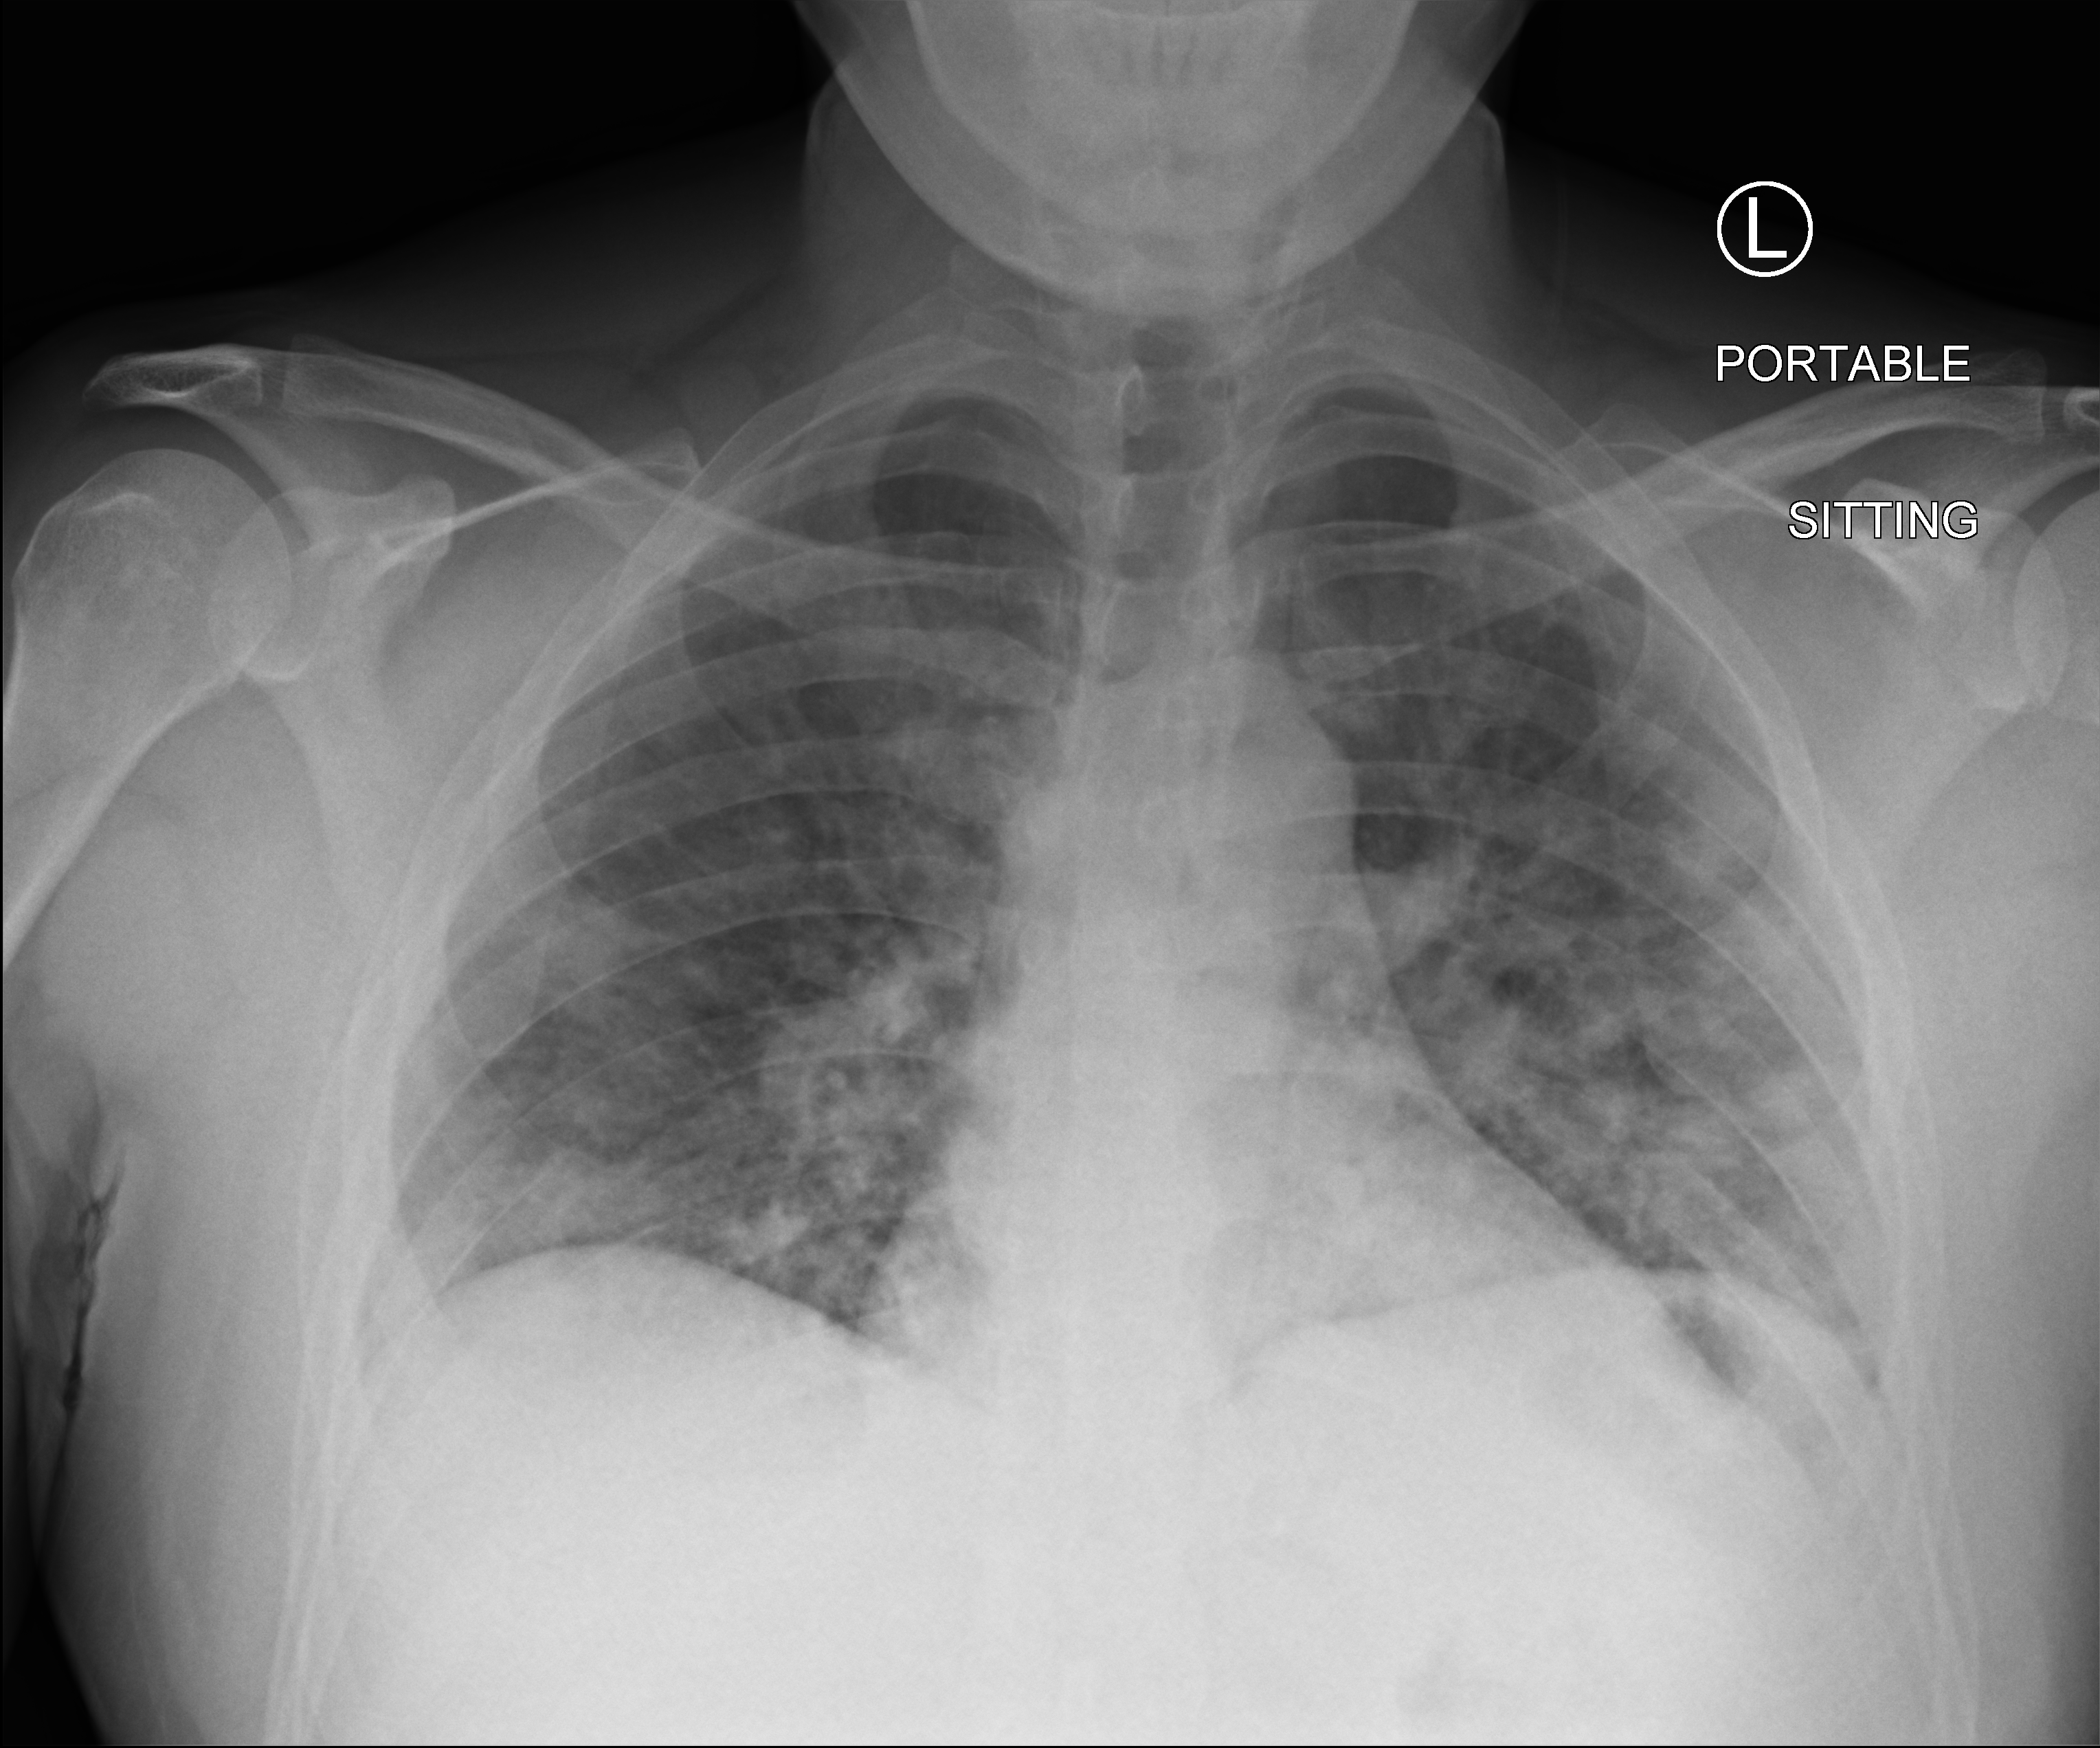
Portable chest radiograph; anteroposterior (AP) projection. Male patient hospitalised with COVID-19, age 18–59 years.
Admission-level facts for this patient (not findings on this image; timing relative to this image not recorded):
- admitted to intensive care during this hospital stay: no
- mechanically ventilated during this hospital stay: no